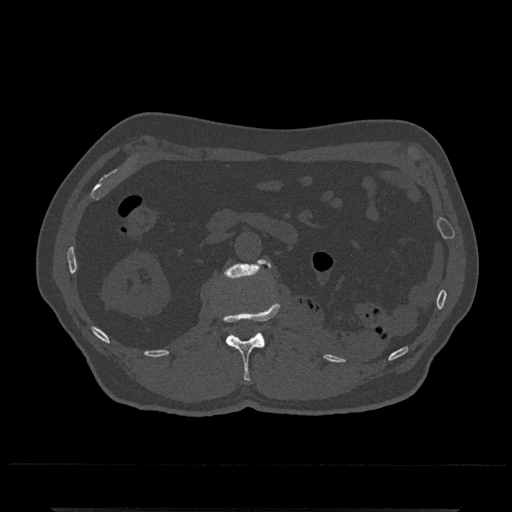
CT including the spine, one axial slice. Position 339 of 797 along the scan axis. Bone window (W 1800 / L 400 HU). 0.5 mm slice thickness. 512 × 512 image matrix, field of view 393 × 393 mm. Male patient, age 67 years. From the clinical record (not read from this slice): primary cancer: prostate.
Structures marked on this image (semi-automatically segmented with operator editing):
- L1 vertebra: bounding box [x1, y1, x2, y2] px = [223, 302, 280, 382]
- L2 vertebra: [224, 259, 271, 279]